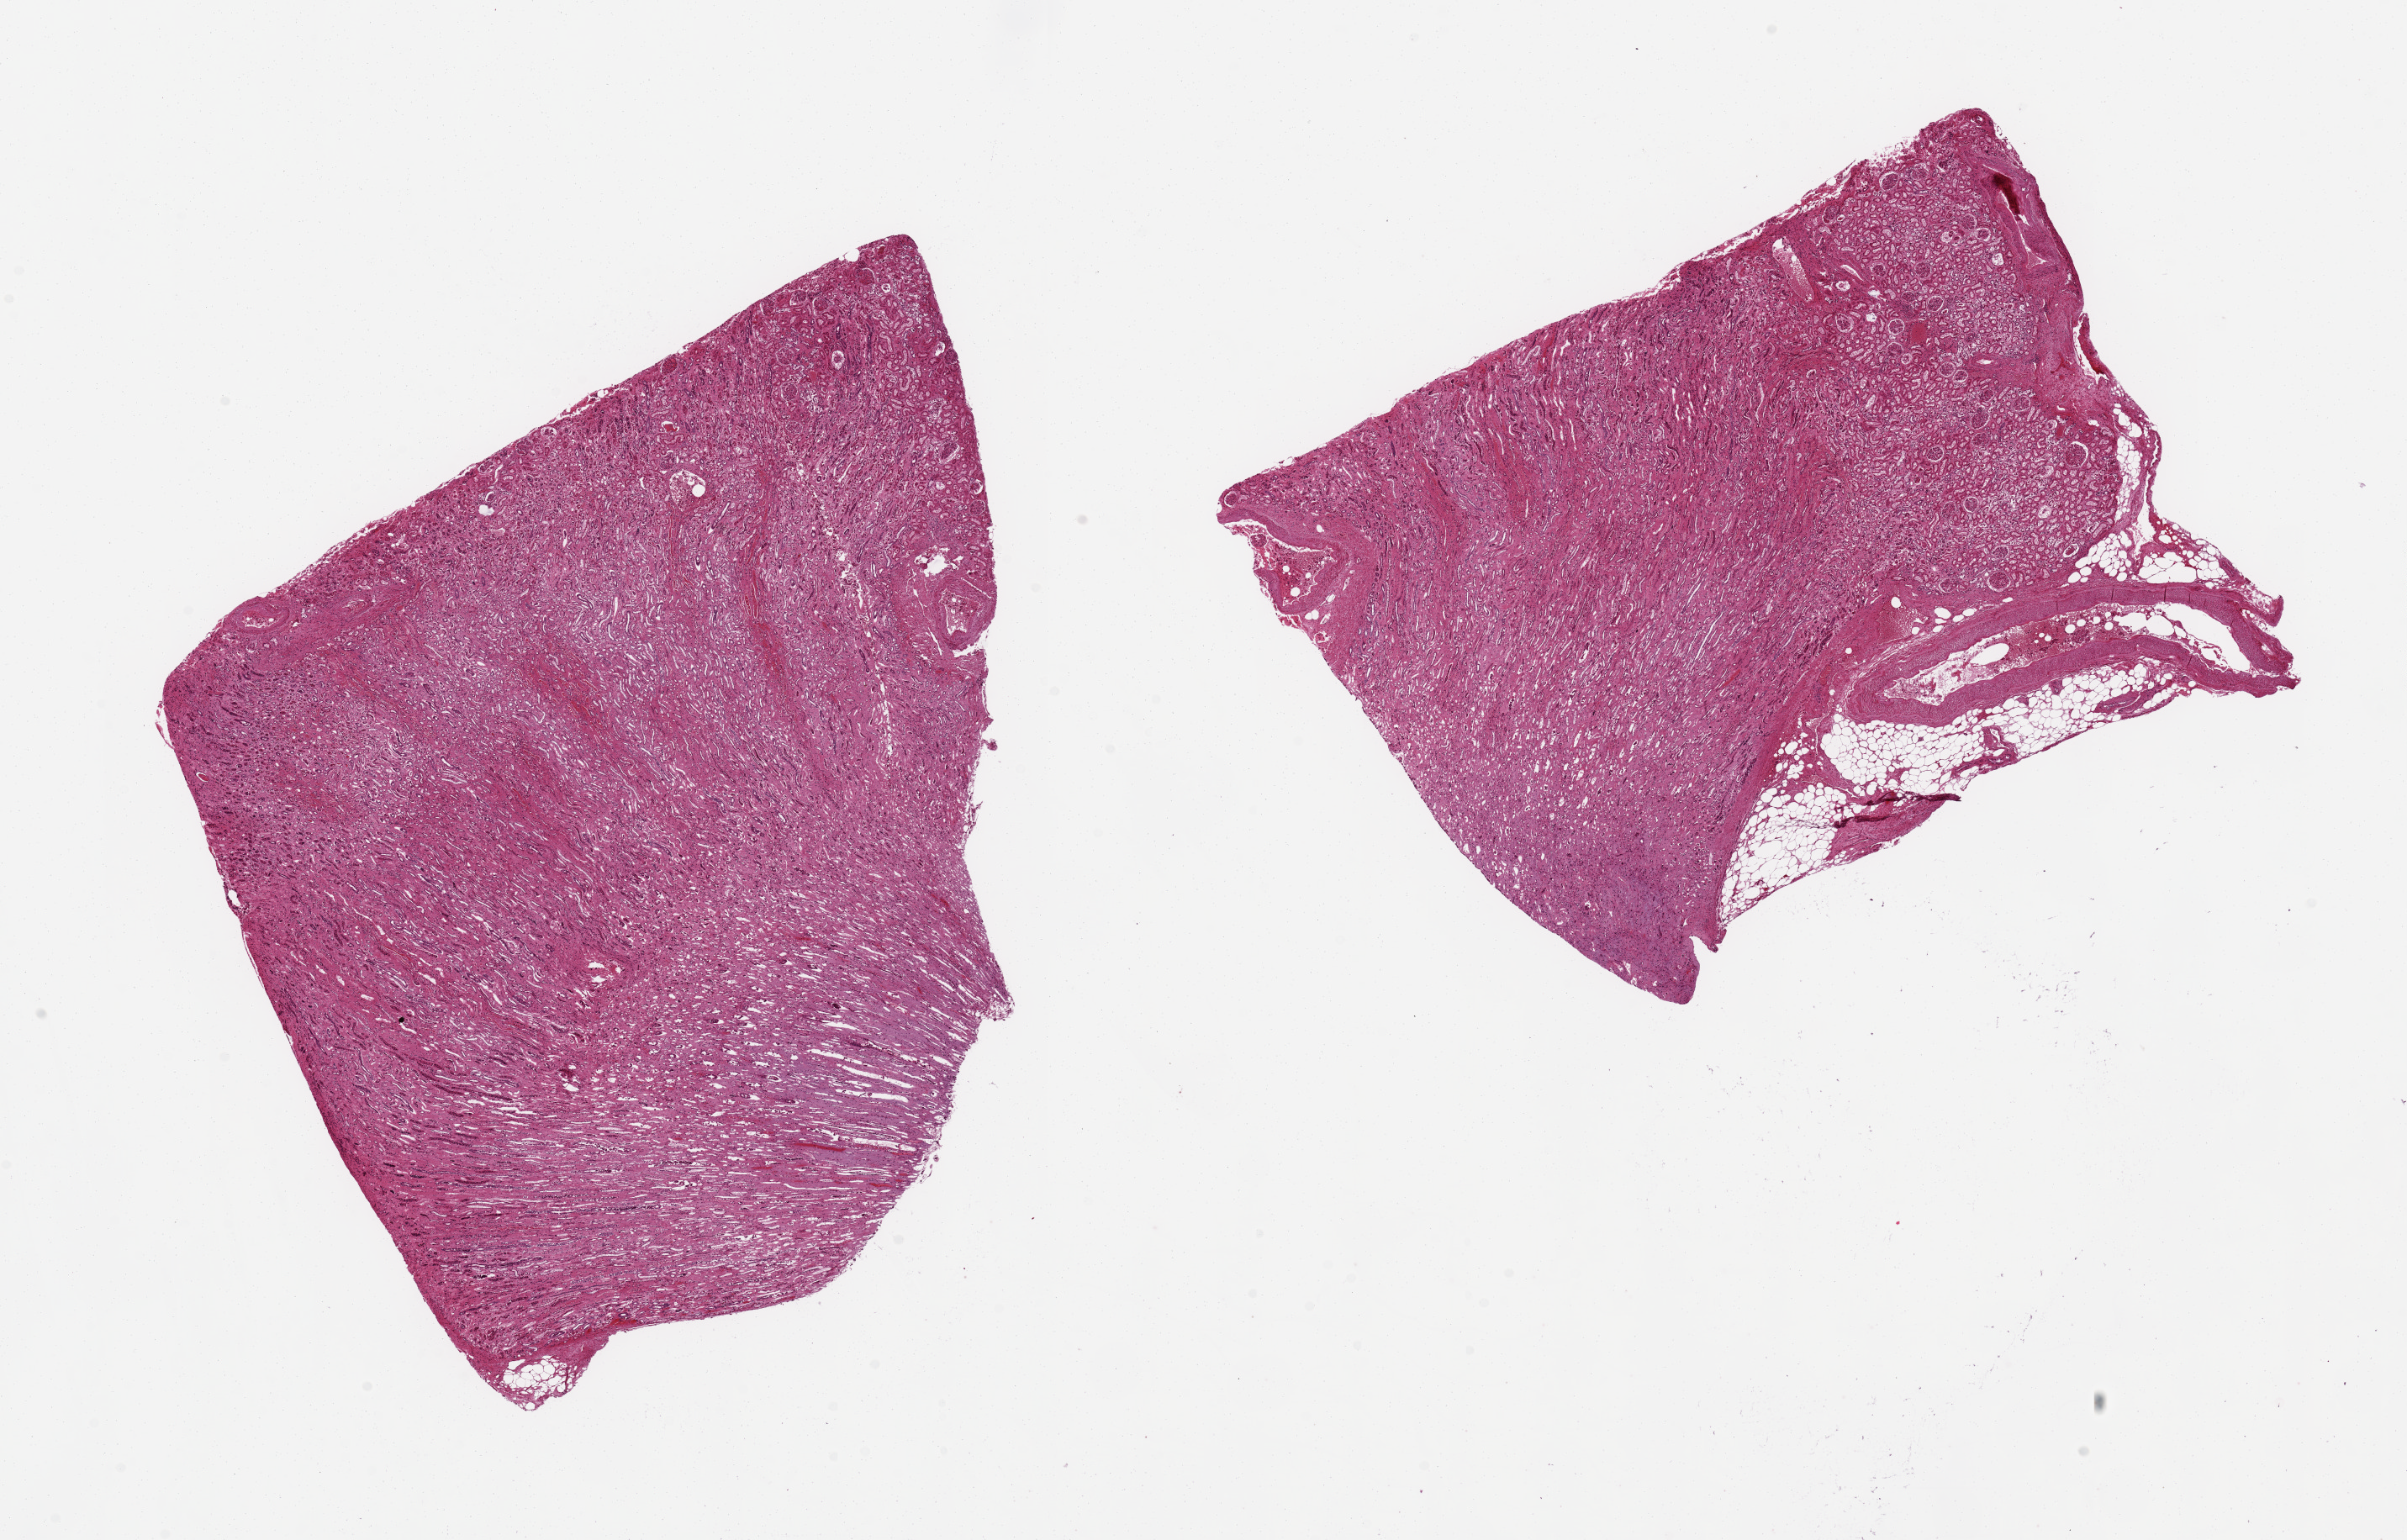
Whole-slide image, hematoxylin and eosin (H&E) stain — a low-resolution overview of the entire scanned area, about 22.6 x 14.5 mm (from a 20x scan). PAXgene-fixed paraffin-embedded (PFPE) section. Section of renal medulla (target tissue). Tissue donor sample. Female donor.
Review note (as recorded): 2 aliquots, ~8x6mm. Minor (~20-30%) 'contamination' by cortex with glomeruli, noted on images.